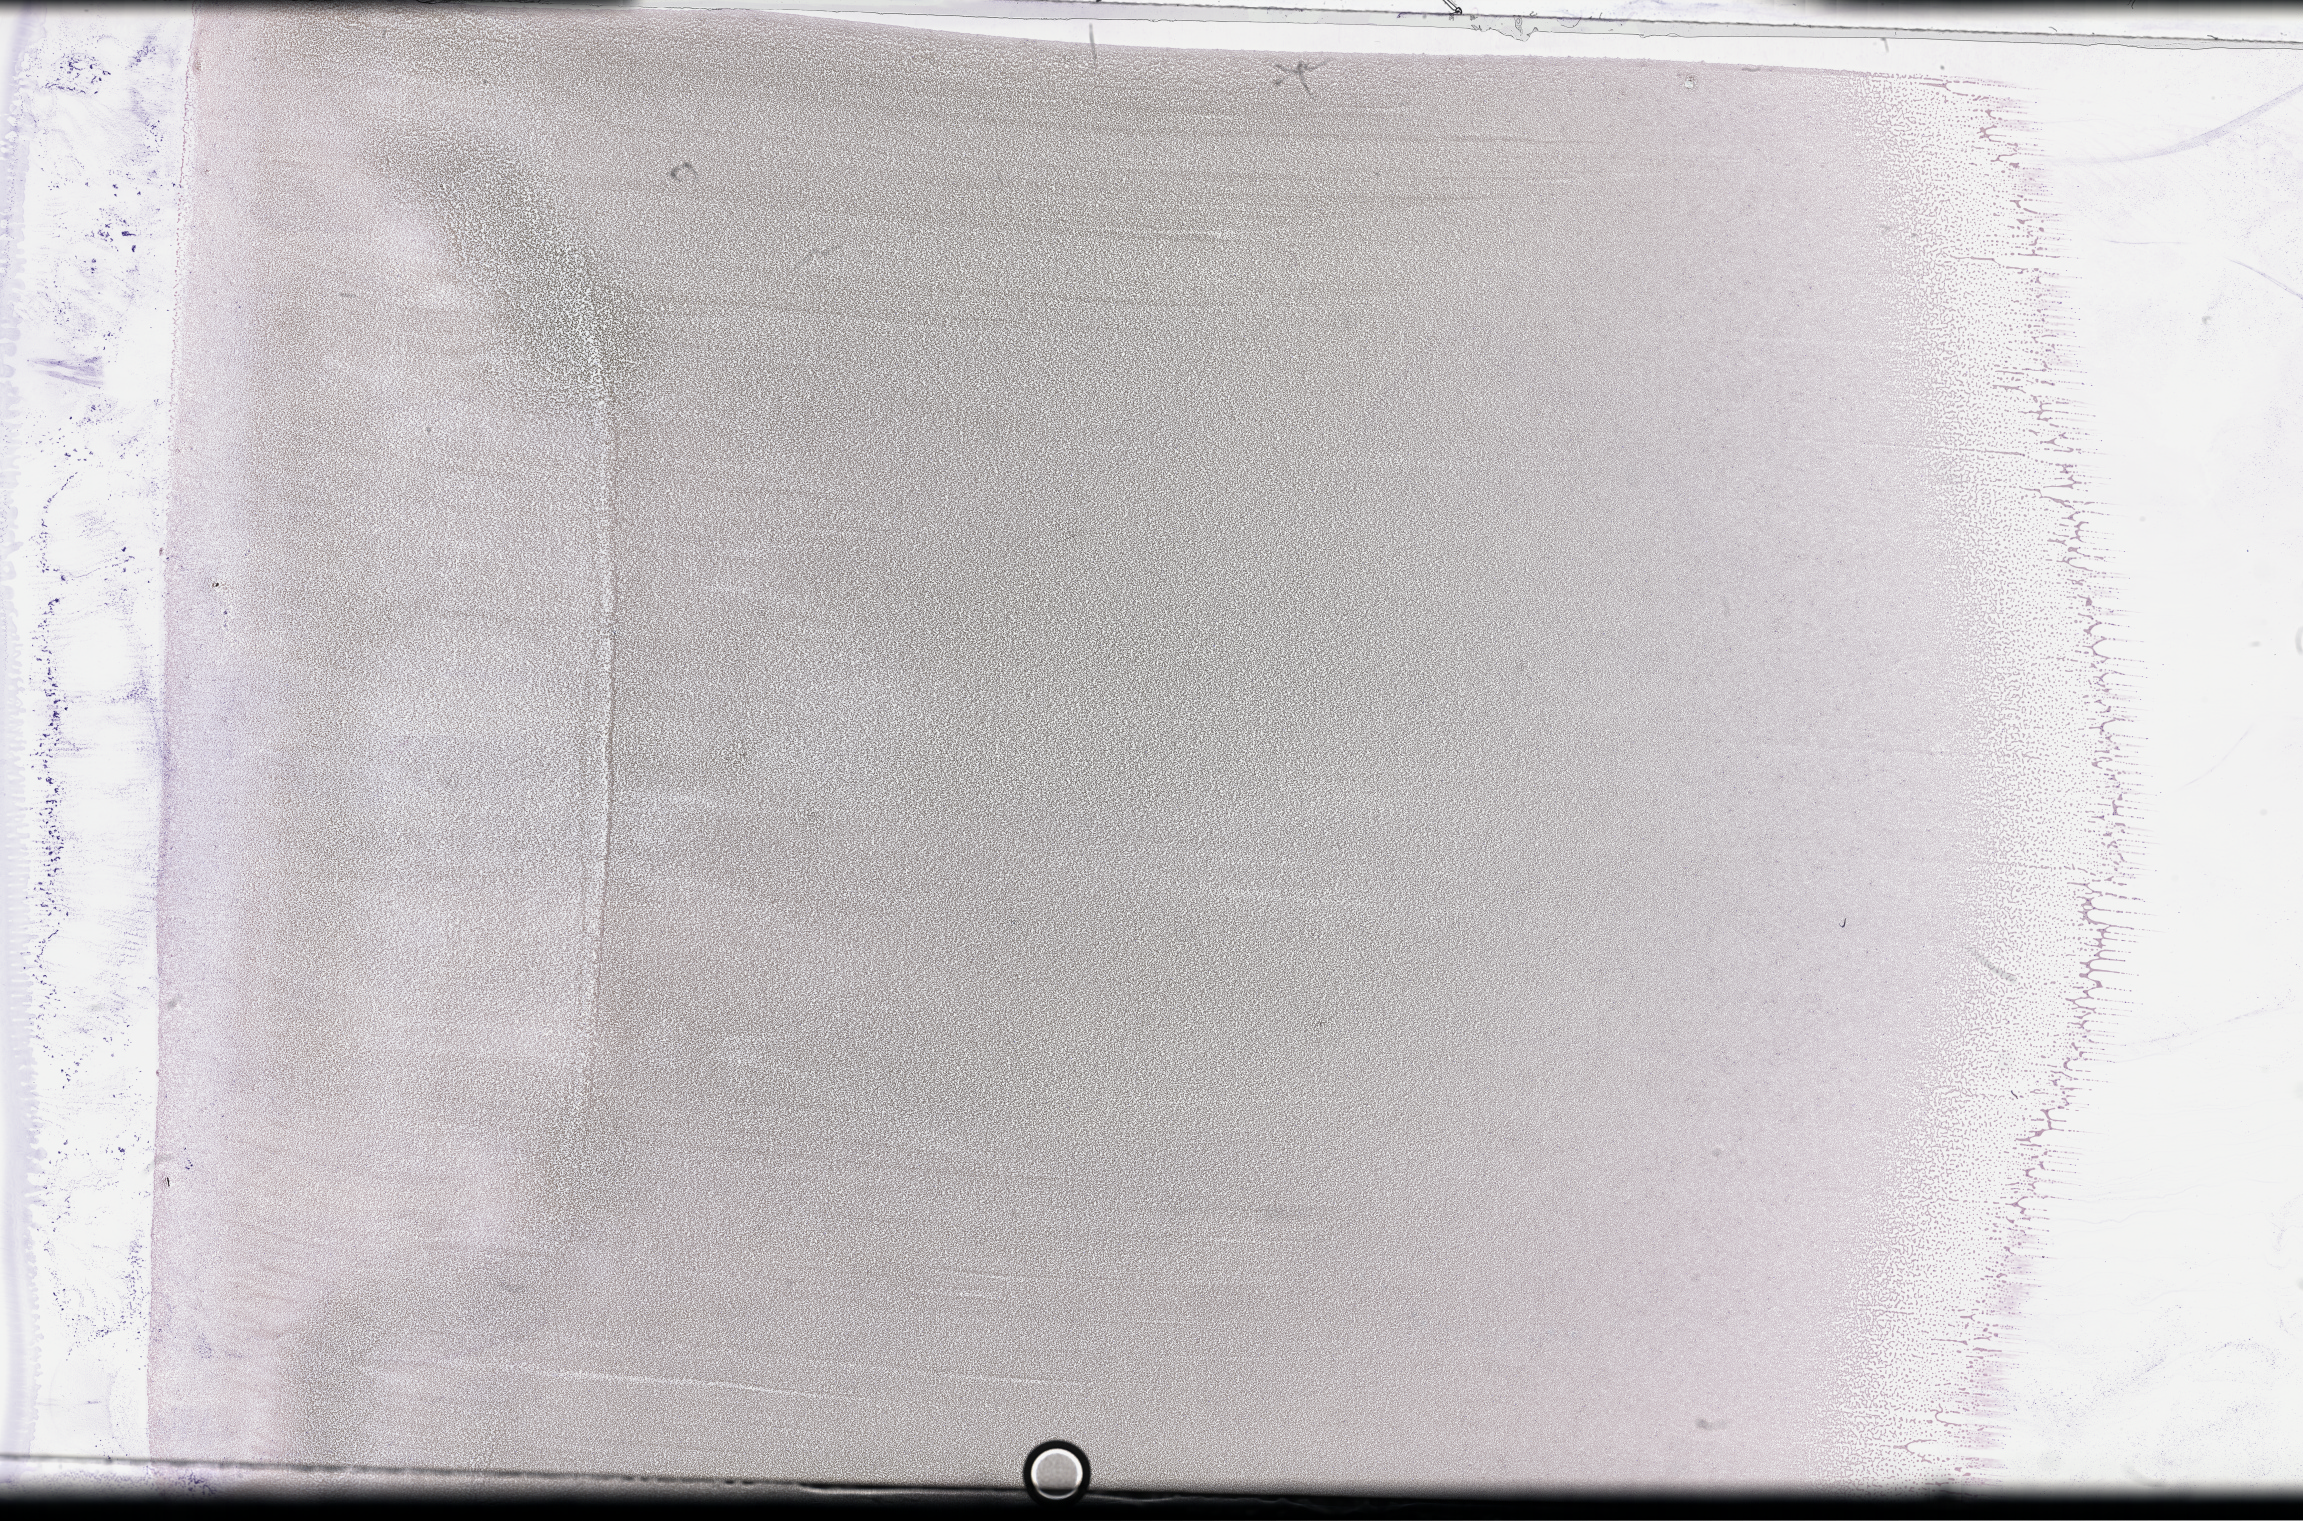
Whole-slide image of a whole blood smear, Wright-Giemsa stain — low-resolution overview of the scanned area, about 37.2 x 24.6 mm, collected on treatment. Patient: female.
• patient diagnosis: Plasma Cell Myeloma